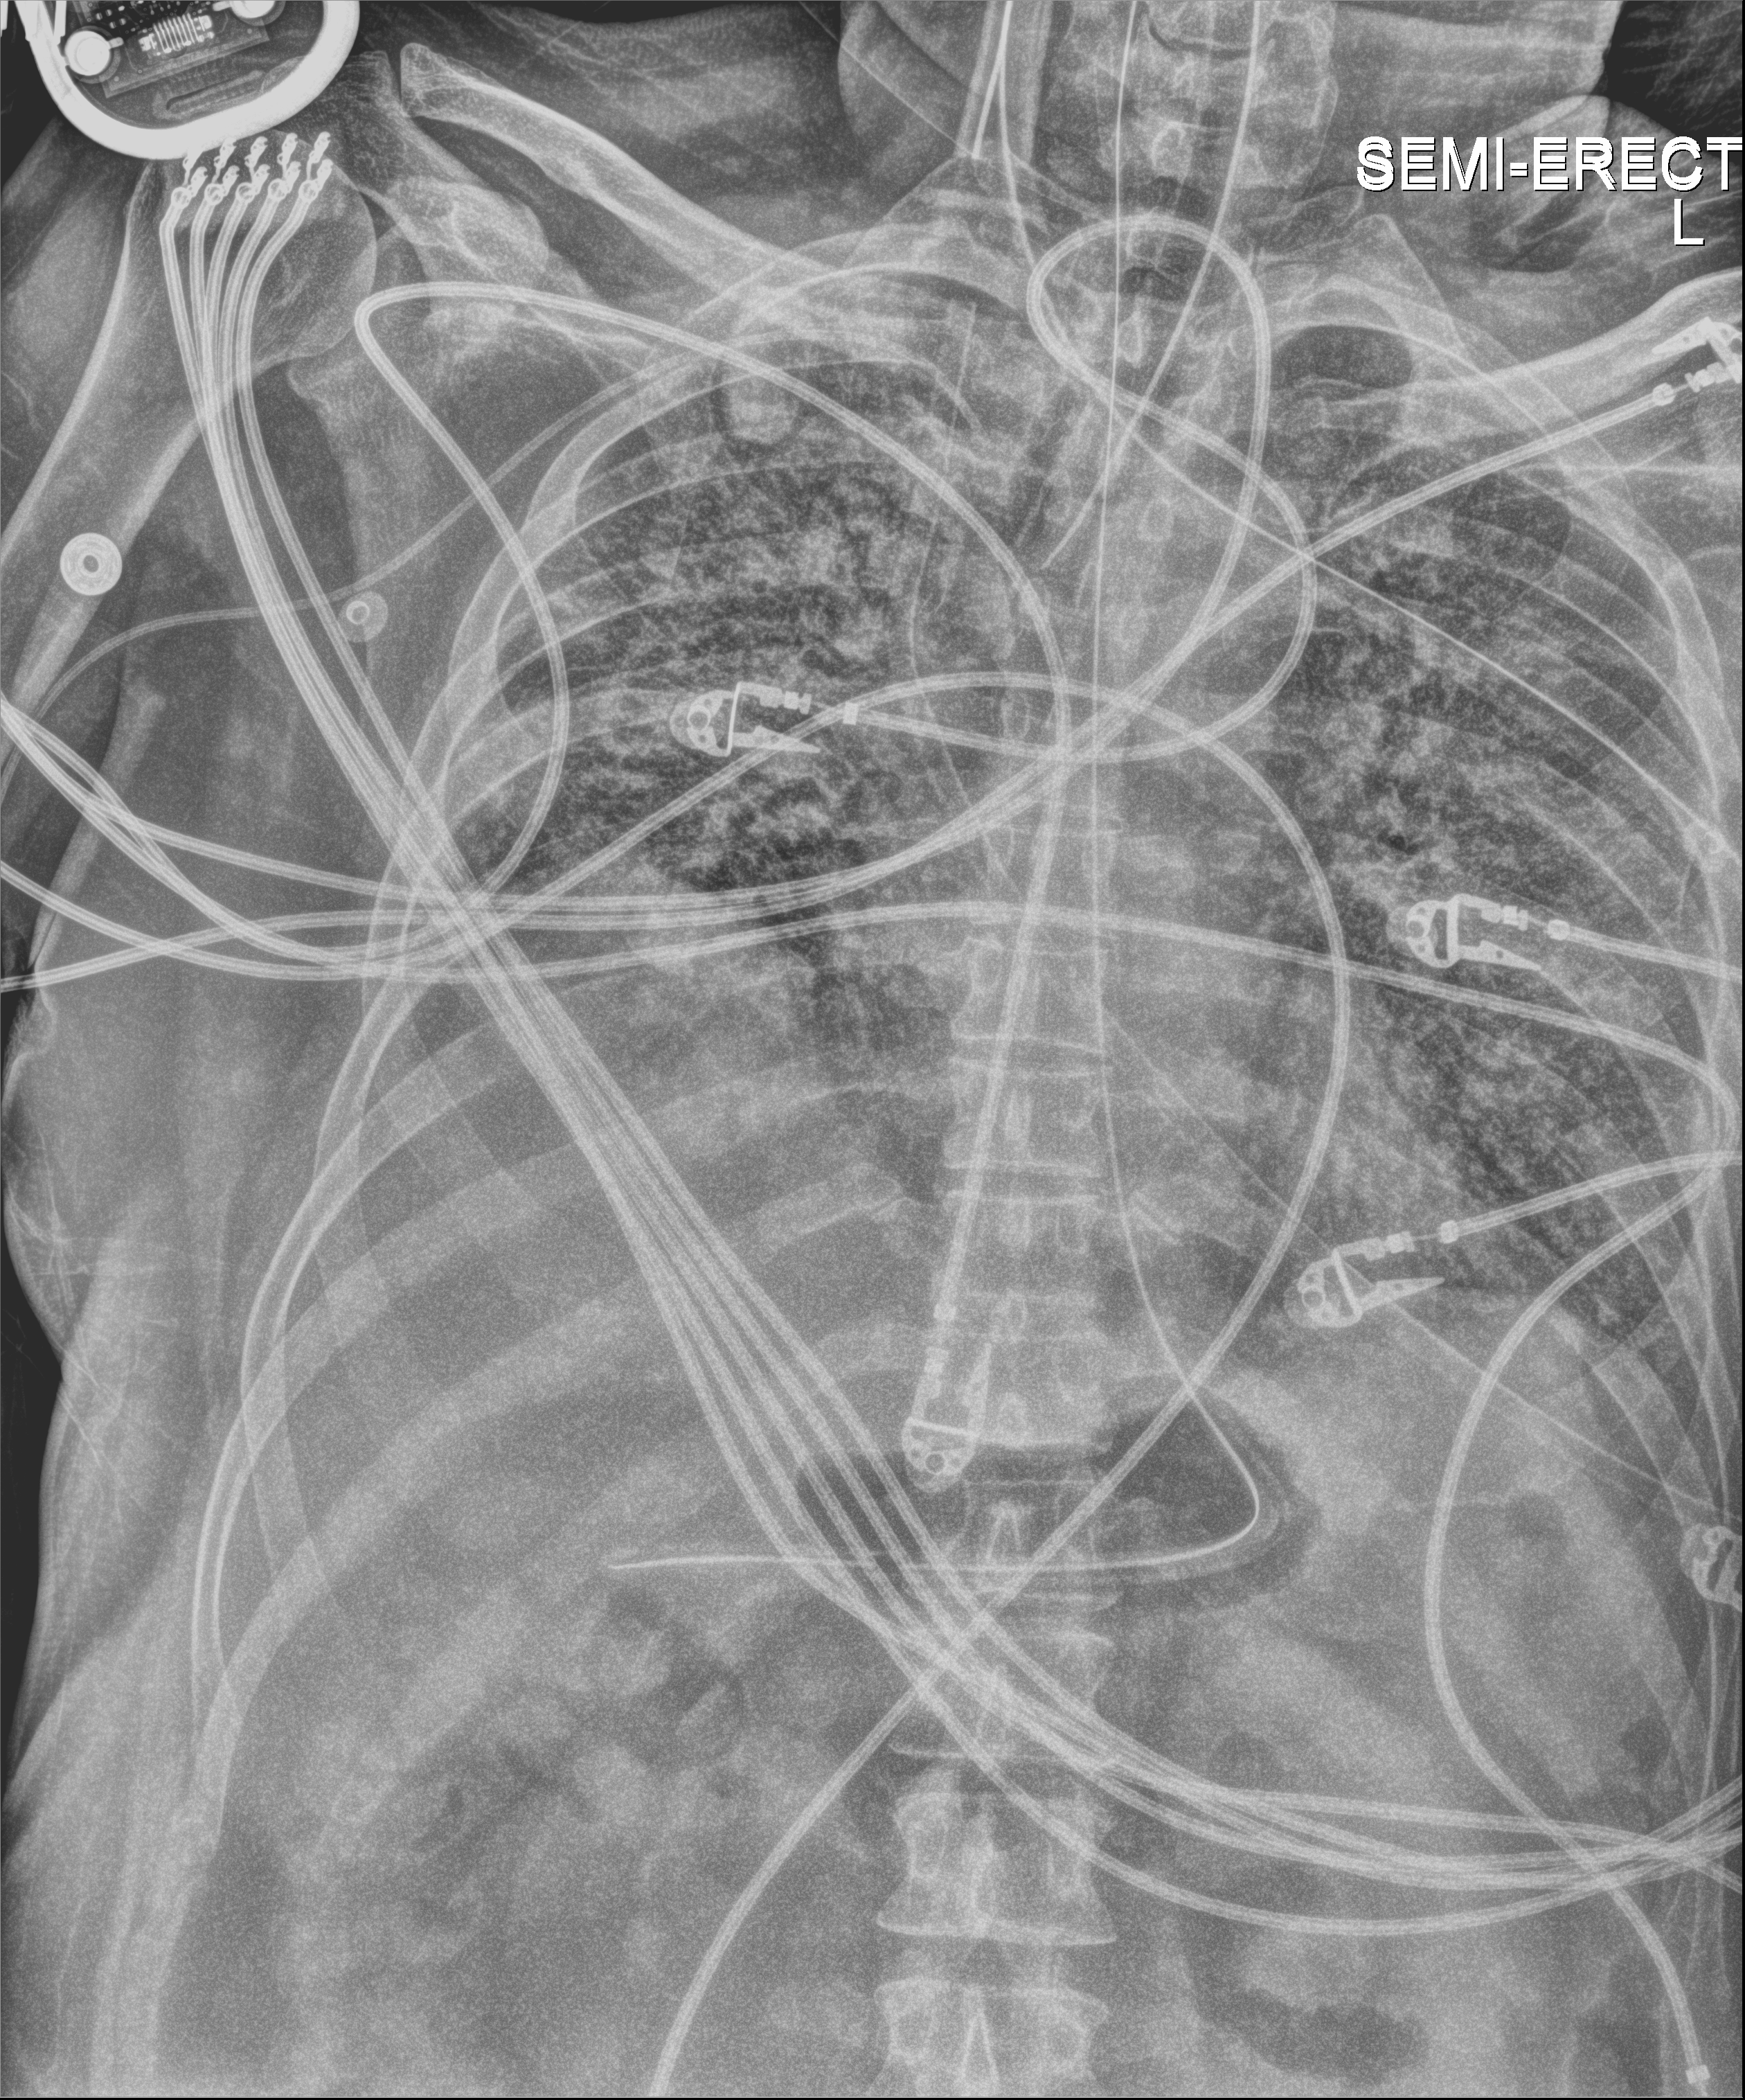
Chest X-ray (portable), anteroposterior (AP) projection. Male patient hospitalised with COVID-19, age 18–59 years.
Hospital-stay facts (about this admission, not read from this image; timing relative to this image not recorded):
- mechanically ventilated during this hospital stay: yes
- admitted to intensive care during this hospital stay: yes